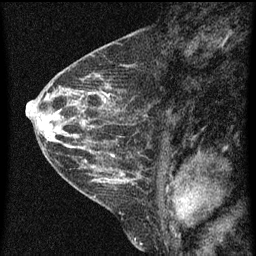
Breast MRI (dynamic contrast-enhanced), one sagittal slice. Dynamic contrast-enhanced series, image 2 of 3 at this slice position (ordered by acquisition). 1.5 T. TE 4.2 ms, TR 8 ms. 2 mm slice thickness. 256 × 256 image matrix. Patient: female, 48 years.
Annotated regions visible in this slice (semi-automatically segmented with operator editing):
- analysis volume of interest (the breast-tissue region the enhancement analysis was run in; not a lesion): bounding box (x1, y1, x2, y2) in pixels: (82, 74, 112, 125)
- tumour enhancement mask (voxels above the 70 % enhancement threshold inside the analysis volume of interest): (103, 92, 110, 101)